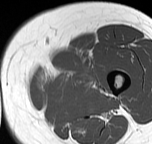
MRI of an extremity soft-tissue mass, one axial slice. Position 13 of 57 along the scan axis. MR volume resampled by the dataset authors to the PET/CT grid (not the native acquisition matrix). 3.27 mm slice thickness. 152 × 144 image matrix, field of view 148 × 141 mm. Female patient. Case-level facts recorded for this patient, not image findings: histological type: pleiomorphic leiomyosarcoma; grade: intermediate; site of the primary tumour: left thigh.
Structures marked on this image (expert contour drawn on MRI and transferred to this co-registered scan by the dataset authors):
- gross tumour volume including surrounding oedema: bounding box (x1, y1, x2, y2) in pixels: (40, 67, 103, 93)